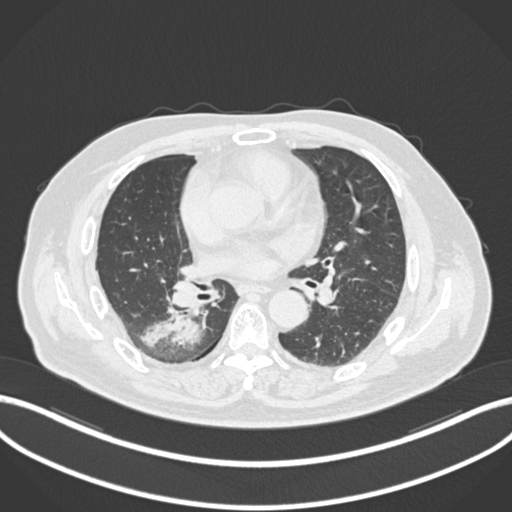
Chest CT, one axial slice; position 94 of 218 along the scan axis; reconstruction kernel B30f; 120 kVp; lung window (W 1500 / L -600 HU); 1 mm slice thickness; 512 × 512 image matrix, field of view 400 × 400 mm. Male patient, age 68 years. Case-level facts recorded for this patient, not image findings: clinical TNM (as recorded): T2a N0 M0.
Annotated regions visible in this slice (rectangle marked by the reading radiologist):
- lung tumour (recorded histology: adenocarcinoma): box from (x=134, y=306) to (x=201, y=355) px